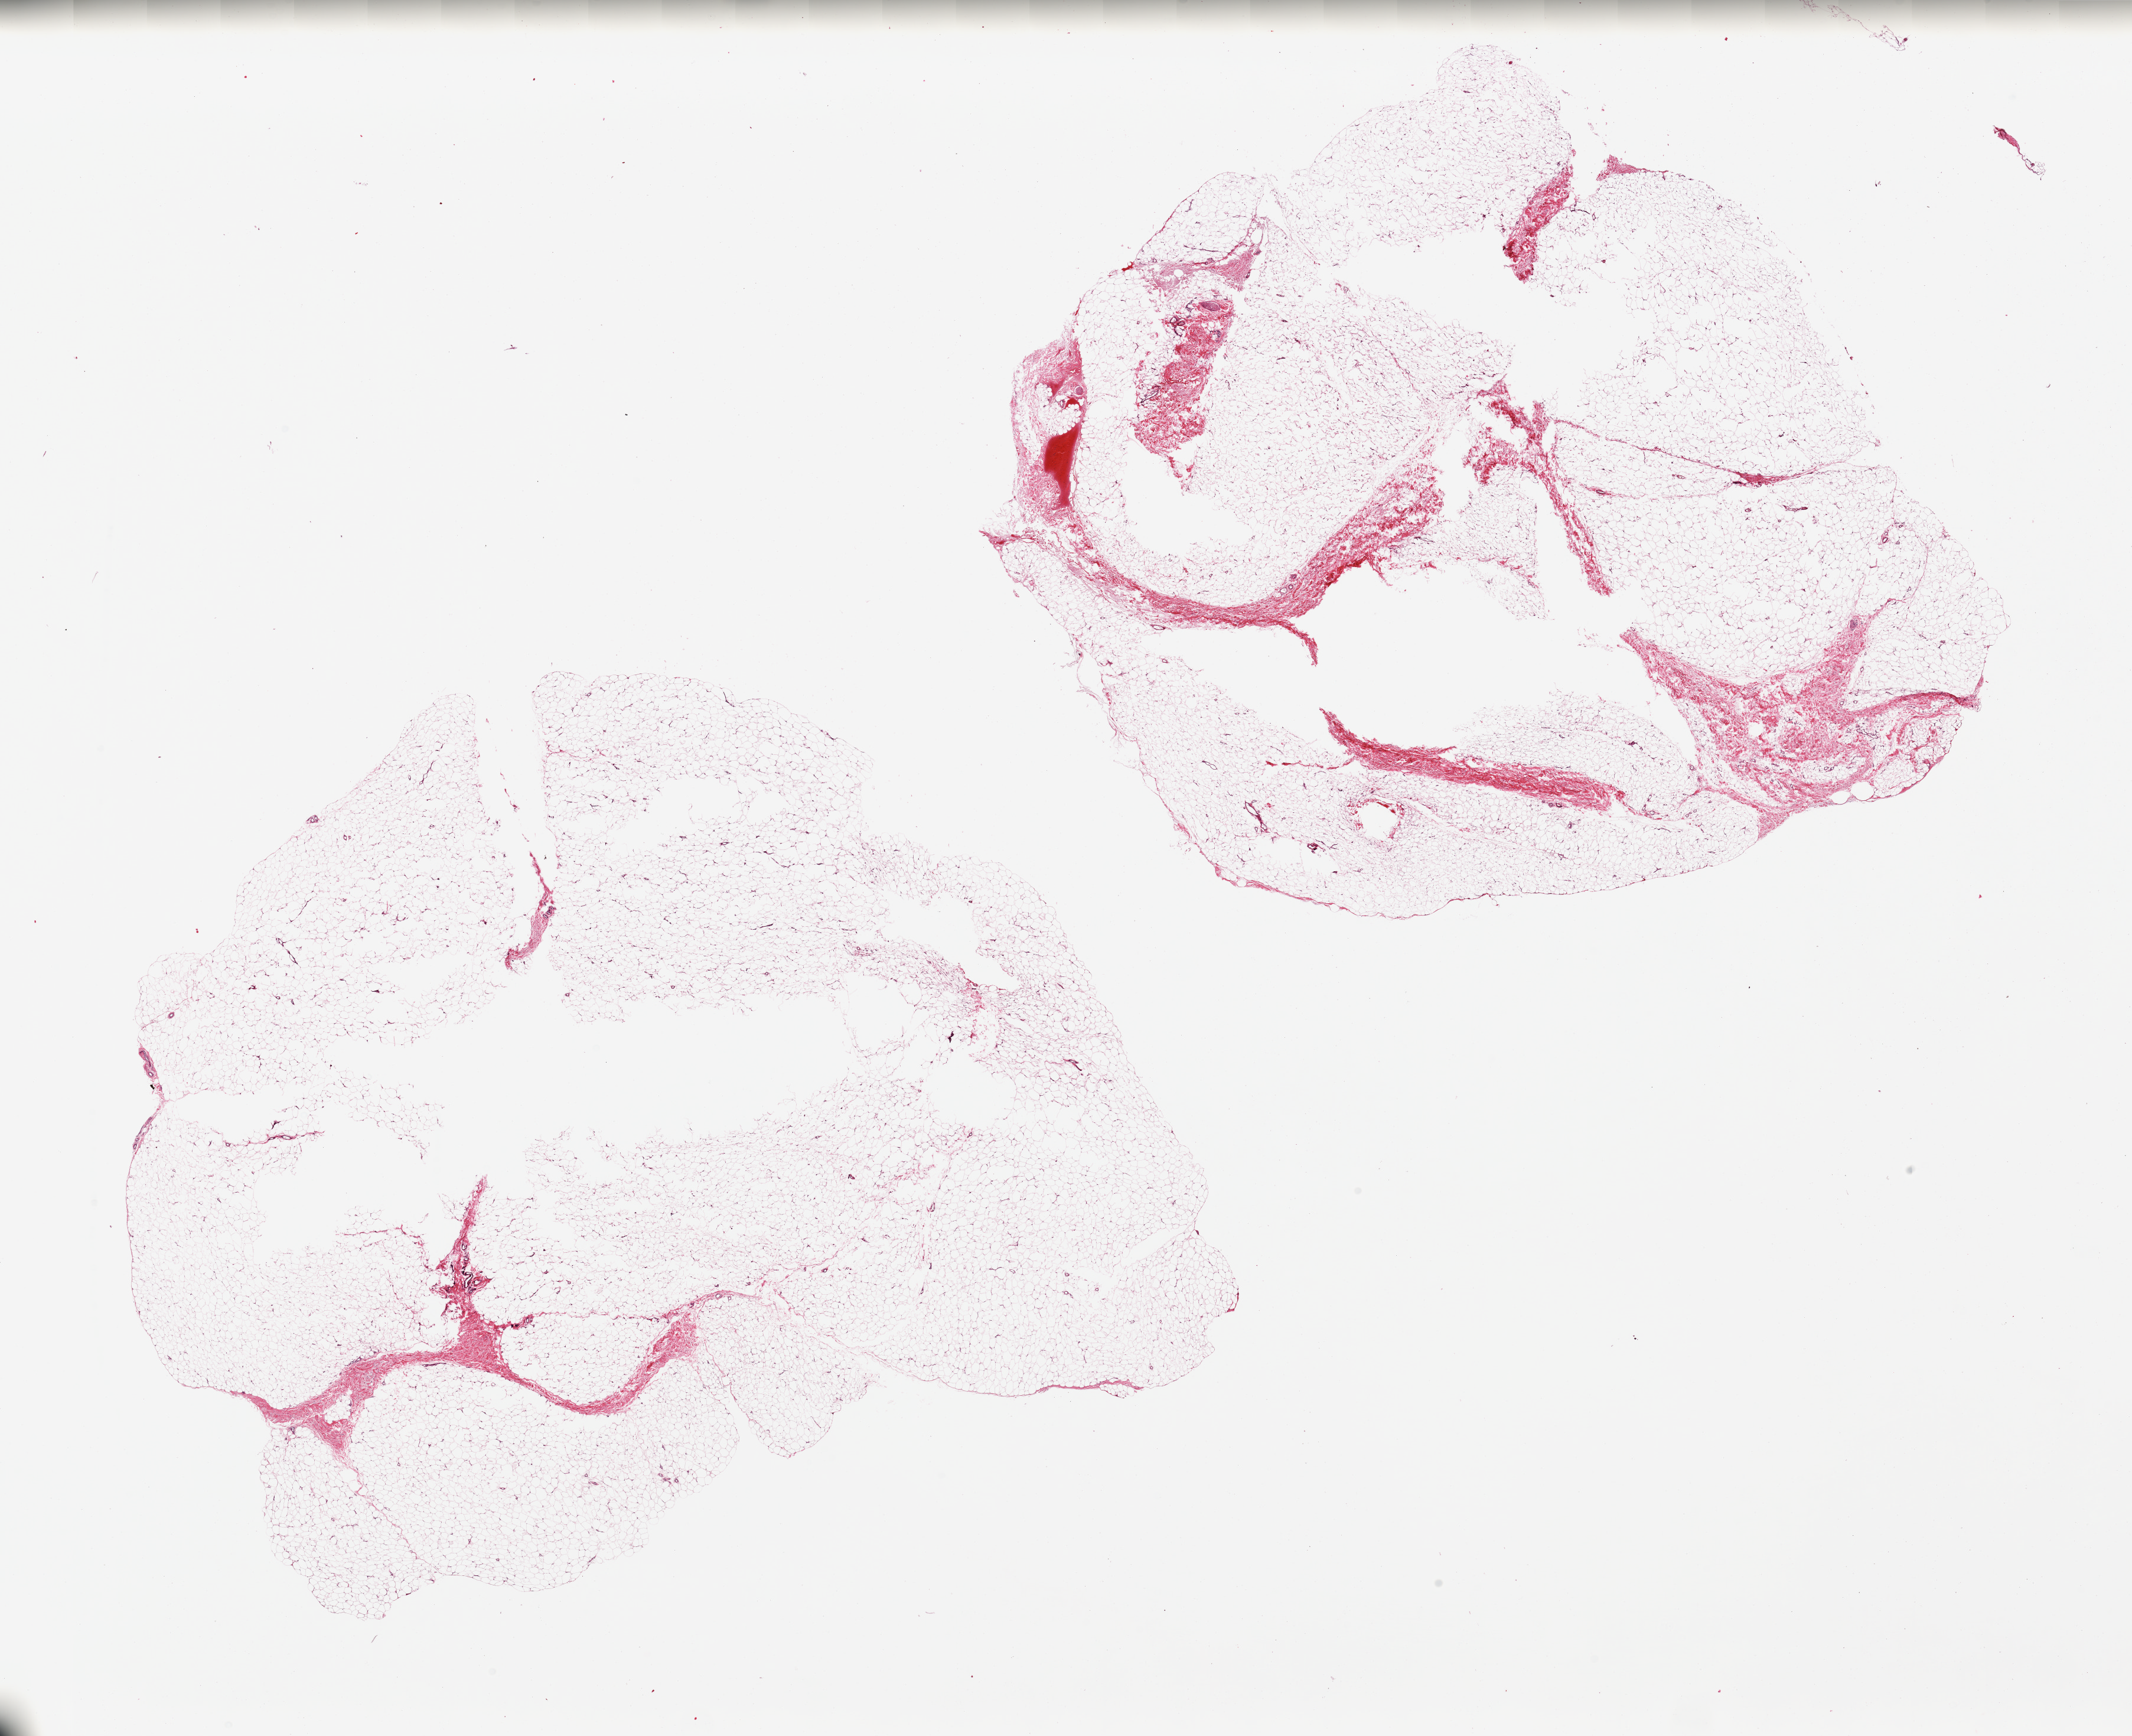
Haematoxylin and eosin whole-slide image, brightfield — low-resolution overview of the scanned area, about 28.5 x 23.2 mm (slide scanned at 20x); PAXgene-fixed, paraffin-embedded tissue; section of adipose tissue (target tissue); tissue donor sample. Donor sex: female.
* review note (as recorded): 2 pieces, ~10% fascia/vessels